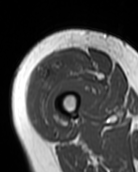
MRI of an extremity soft-tissue mass, one axial slice. Position 26 of 99 along the scan axis. MR volume resampled by the dataset authors to the PET/CT grid (not the native acquisition matrix). 3.27 mm slice thickness. 138 × 172 image matrix, field of view 135 × 168 mm. Female patient. From the clinical record (not read from this slice): histological type: pleiomorphic undifferentiated sarcoma; grade: high; site of the primary tumour: right quadricep.
Outlined on this slice (expert contour drawn on MRI and transferred to this co-registered scan by the dataset authors):
- gross tumour volume including surrounding oedema: bounding box <30,50,100,124> (left, top, right, bottom; pixels)